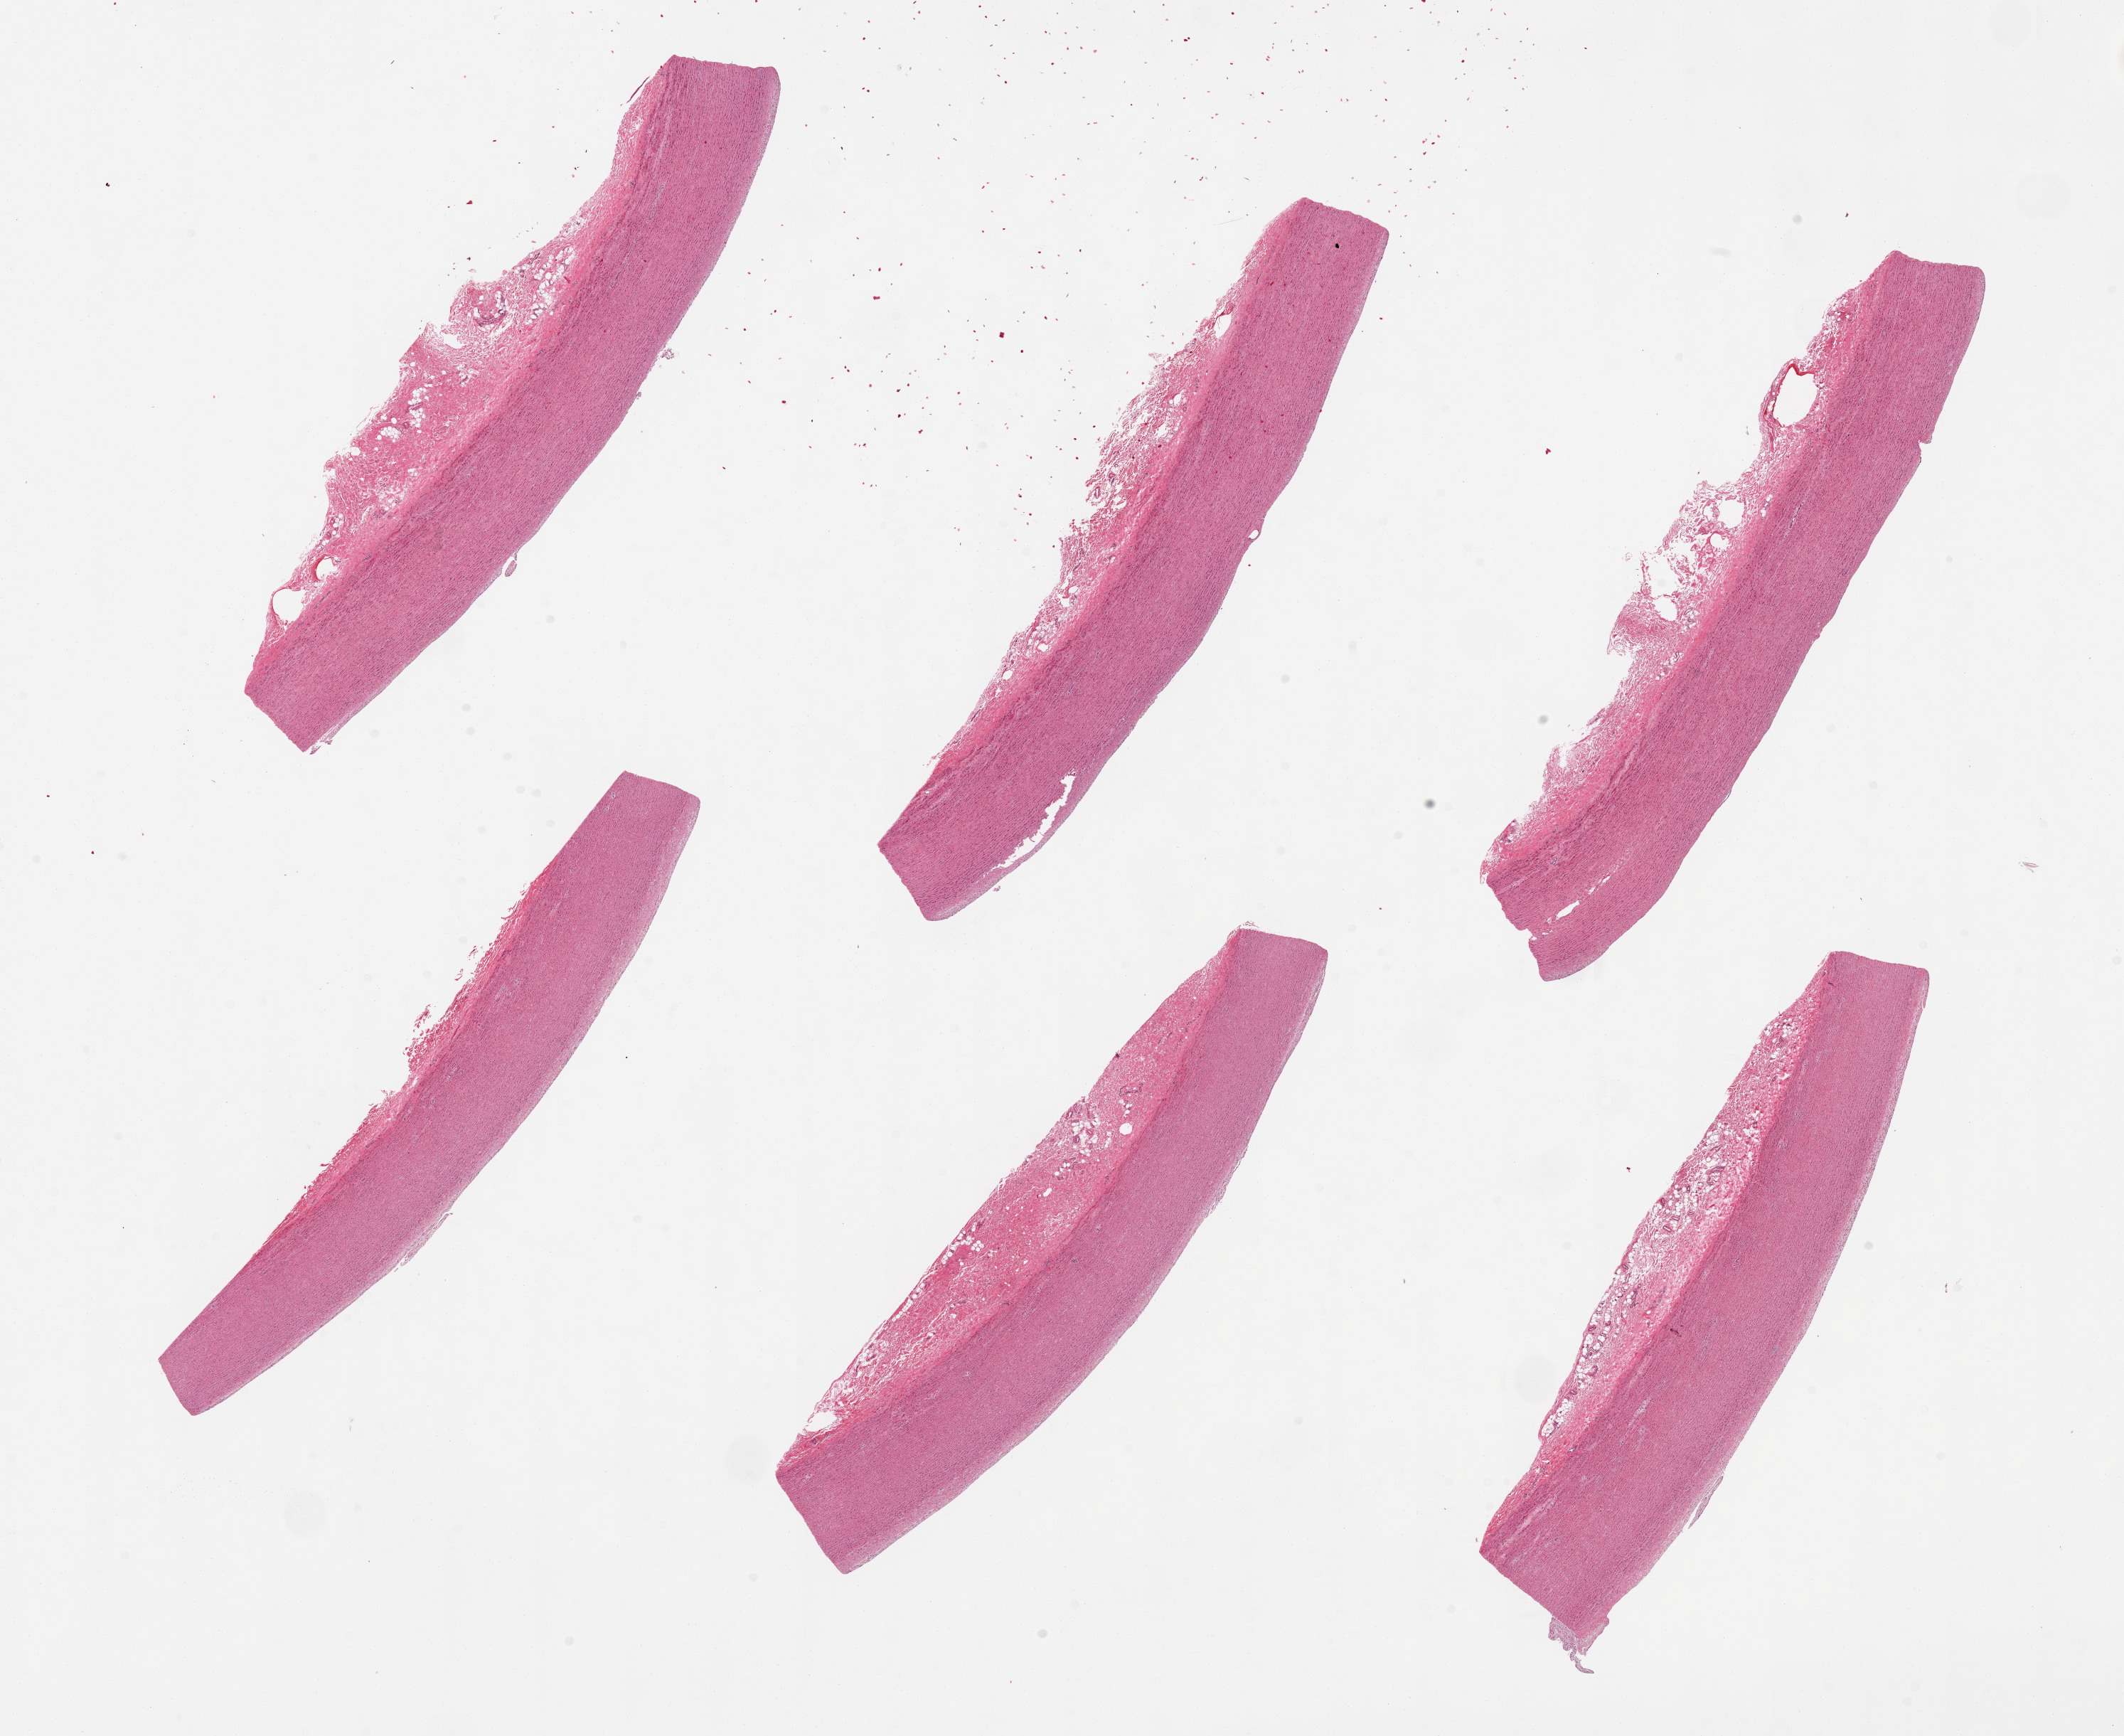
Hematoxylin and eosin (H&E) whole-slide image, whole scanned area (about 23.6 x 19.3 mm, acquisition: 20x scan) shown as a low-resolution overview. PAXgene-fixed, paraffin-embedded tissue. Target tissue: aorta. Donor tissue sample. Male donor.
Review note (as recorded): 6 pieces; no plaques; fibrous adventitia up to 1 mm.